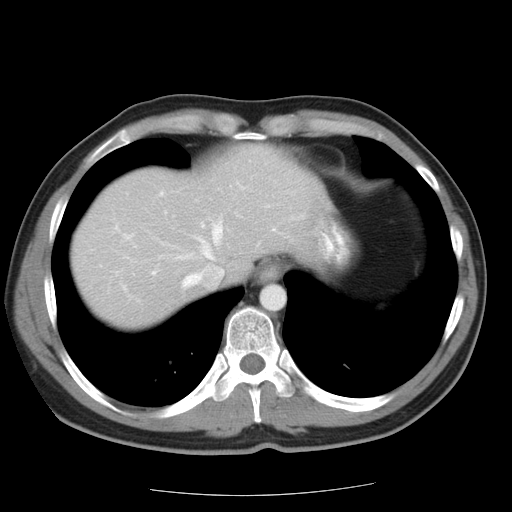
Contrast-enhanced abdominal CT, one axial slice; slice 19 of 22 in the series (ordered by position); 120 kVp; intravenous contrast given; soft-tissue window (W 400 / L 40 HU); 7.5 mm slice thickness; 512 × 512 image matrix, field of view 359 × 359 mm. Male patient, age 41 years. Case-level facts recorded for this patient, not image findings: diagnosis: colorectal cancer liver metastases, imaged before liver resection; multiple liver metastases: no; largest metastasis: 2.7 cm; disease in both lobes: no.
Structures marked on this image (outlined manually by an expert reader):
- hepatic veins: bounding box <184,224,223,287> (left, top, right, bottom; pixels)
- liver: <72,149,309,327>
- planned liver remnant (the part of the liver to remain after resection): <72,148,309,322>
- portal vein (with intrahepatic branches): <126,193,164,238>